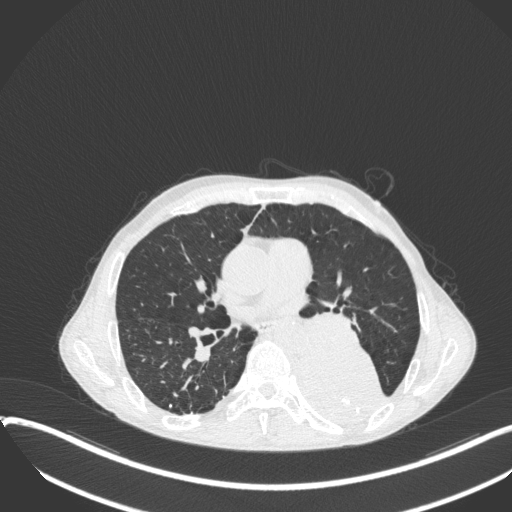
Chest CT, one axial slice; position 197 of 400 along the scan axis; 120 kVp; lung window (W 1500 / L -600 HU); 1 mm slice thickness; 512 × 512 image matrix, field of view 400 × 400 mm. Male patient, age 57 years. From the clinical record (not read from this slice): clinical TNM (as recorded): T4 N0 M0.
Structures marked on this image (rectangle marked by the reading radiologist):
- lung tumour (recorded histology: squamous cell carcinoma): bounding box (x1, y1, x2, y2) in pixels: (288, 332, 390, 430)